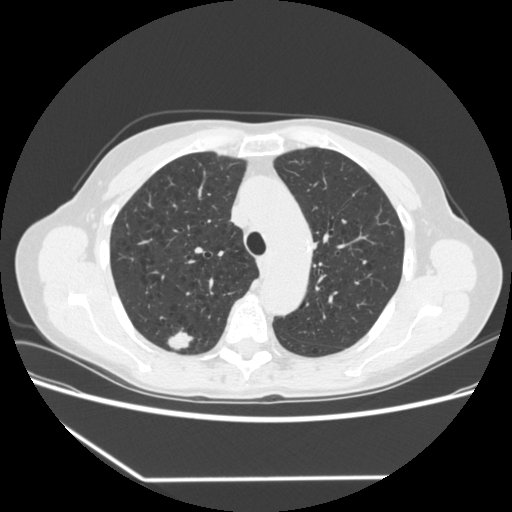
Low-dose screening chest CT, one axial slice; position 245 of 323 along the scan axis; 120 kVp; lung window (W 1500 / L -600 HU); 1.25 mm slice thickness; 512 × 512 image matrix, field of view 360 × 360 mm.
Outlined on this slice (outlined manually by an expert reader):
- lesion 1 (tumor, upper lobe of right lung): bounding box (x1, y1, x2, y2) in pixels: (168, 328, 193, 350)